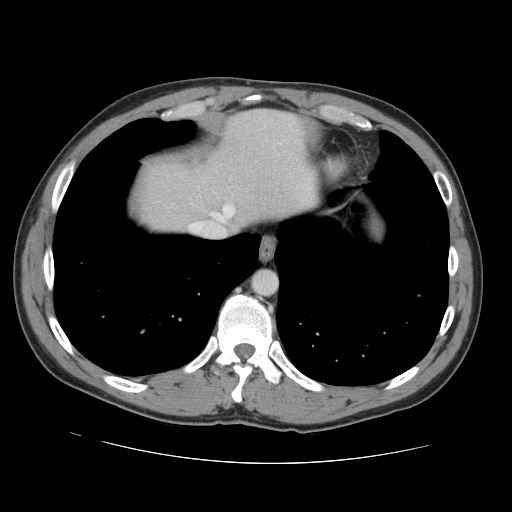
Contrast-enhanced abdominal CT, one axial slice; position 125 of 131 along the scan axis; intravenous contrast given; soft-tissue window (W 400 / L 40 HU); 2.5 mm slice thickness; 512 × 512 image matrix, field of view 380 × 380 mm. Male patient, age 40 years. From the clinical record (not read from this slice): diagnosis: colorectal cancer liver metastases, imaged before liver resection; multiple liver metastases: yes; largest metastasis: 2.9 cm; disease in both lobes: yes.
Annotated regions visible in this slice (outlined manually by an expert reader):
- hepatic veins: bounding box [x1, y1, x2, y2] px = [190, 205, 234, 235]
- liver: [140, 110, 310, 232]
- planned liver remnant (the part of the liver to remain after resection): [144, 110, 312, 229]